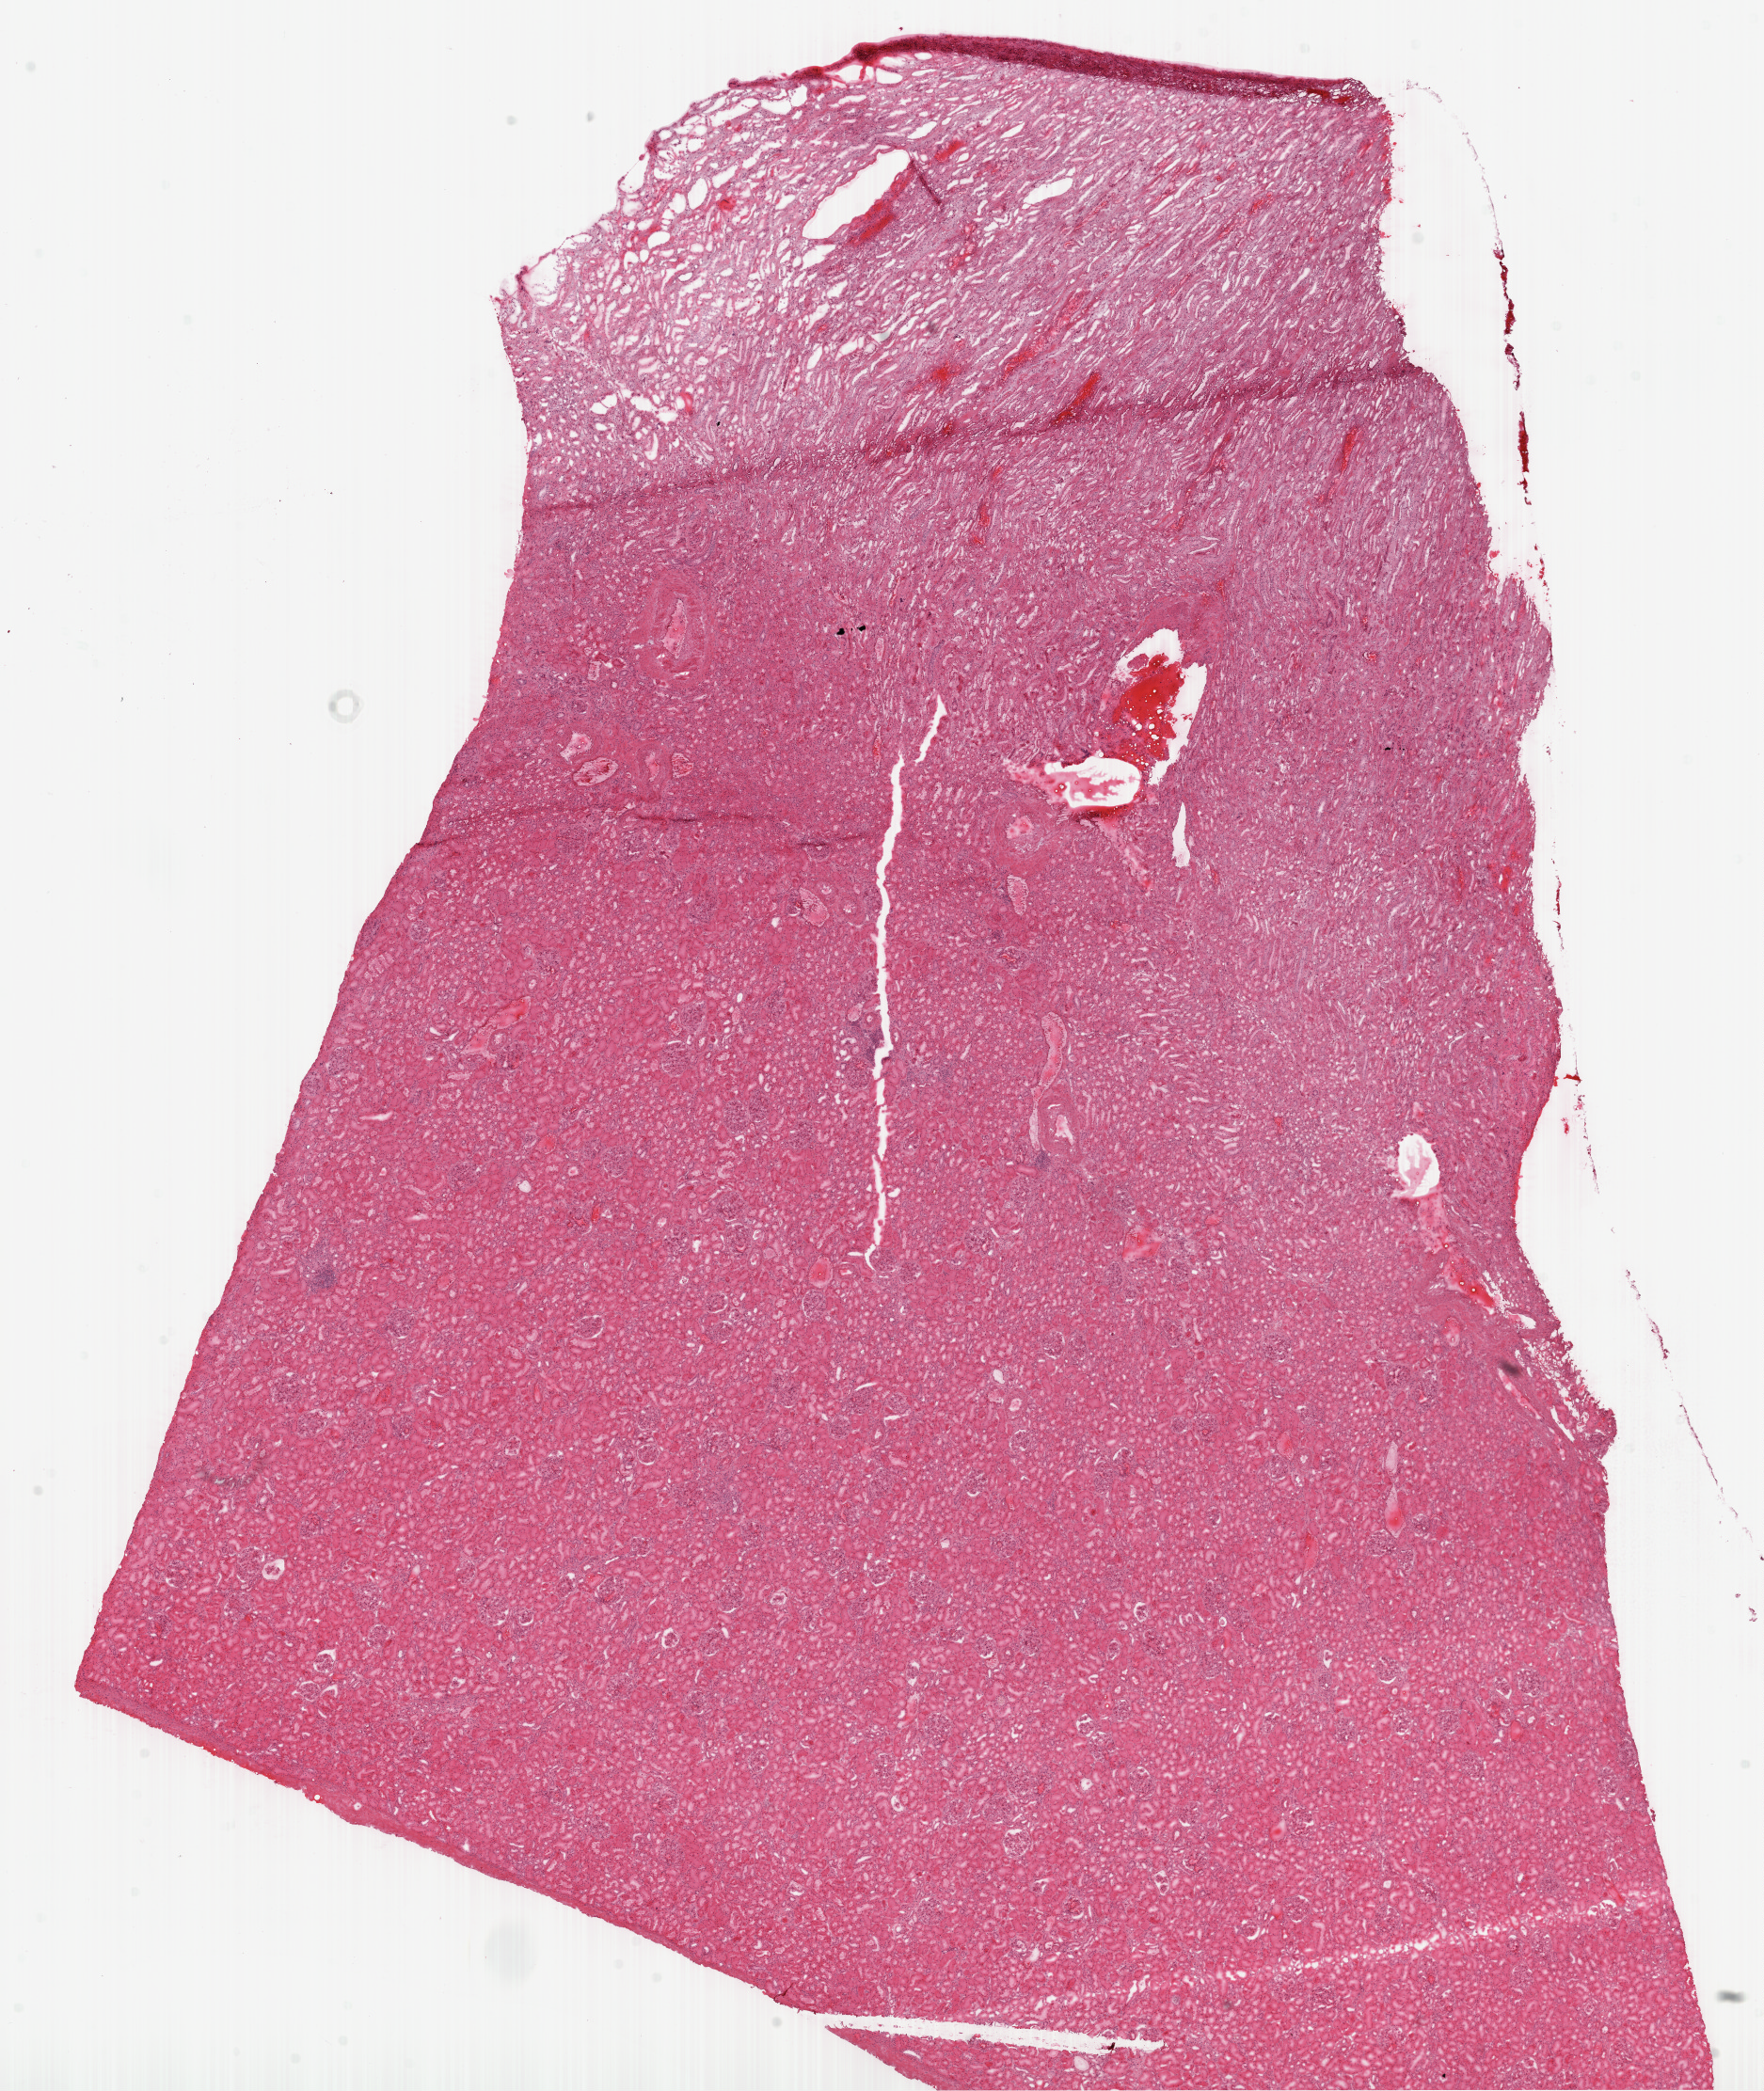
Hematoxylin and eosin (H&E) stained whole-slide image — whole scanned area (about 15.0 x 17.8 mm, from a 20x scan) shown as a low-resolution overview; frozen section from the top of the tissue portion; kidney, solid tissue normal (non-tumour tissue) sample. Patient: male, age at initial diagnosis 57 years.
This section: solid tissue normal (non-tumour) sample from the same patient. Patient diagnosis: Clear cell adenocarcinoma, NOS.